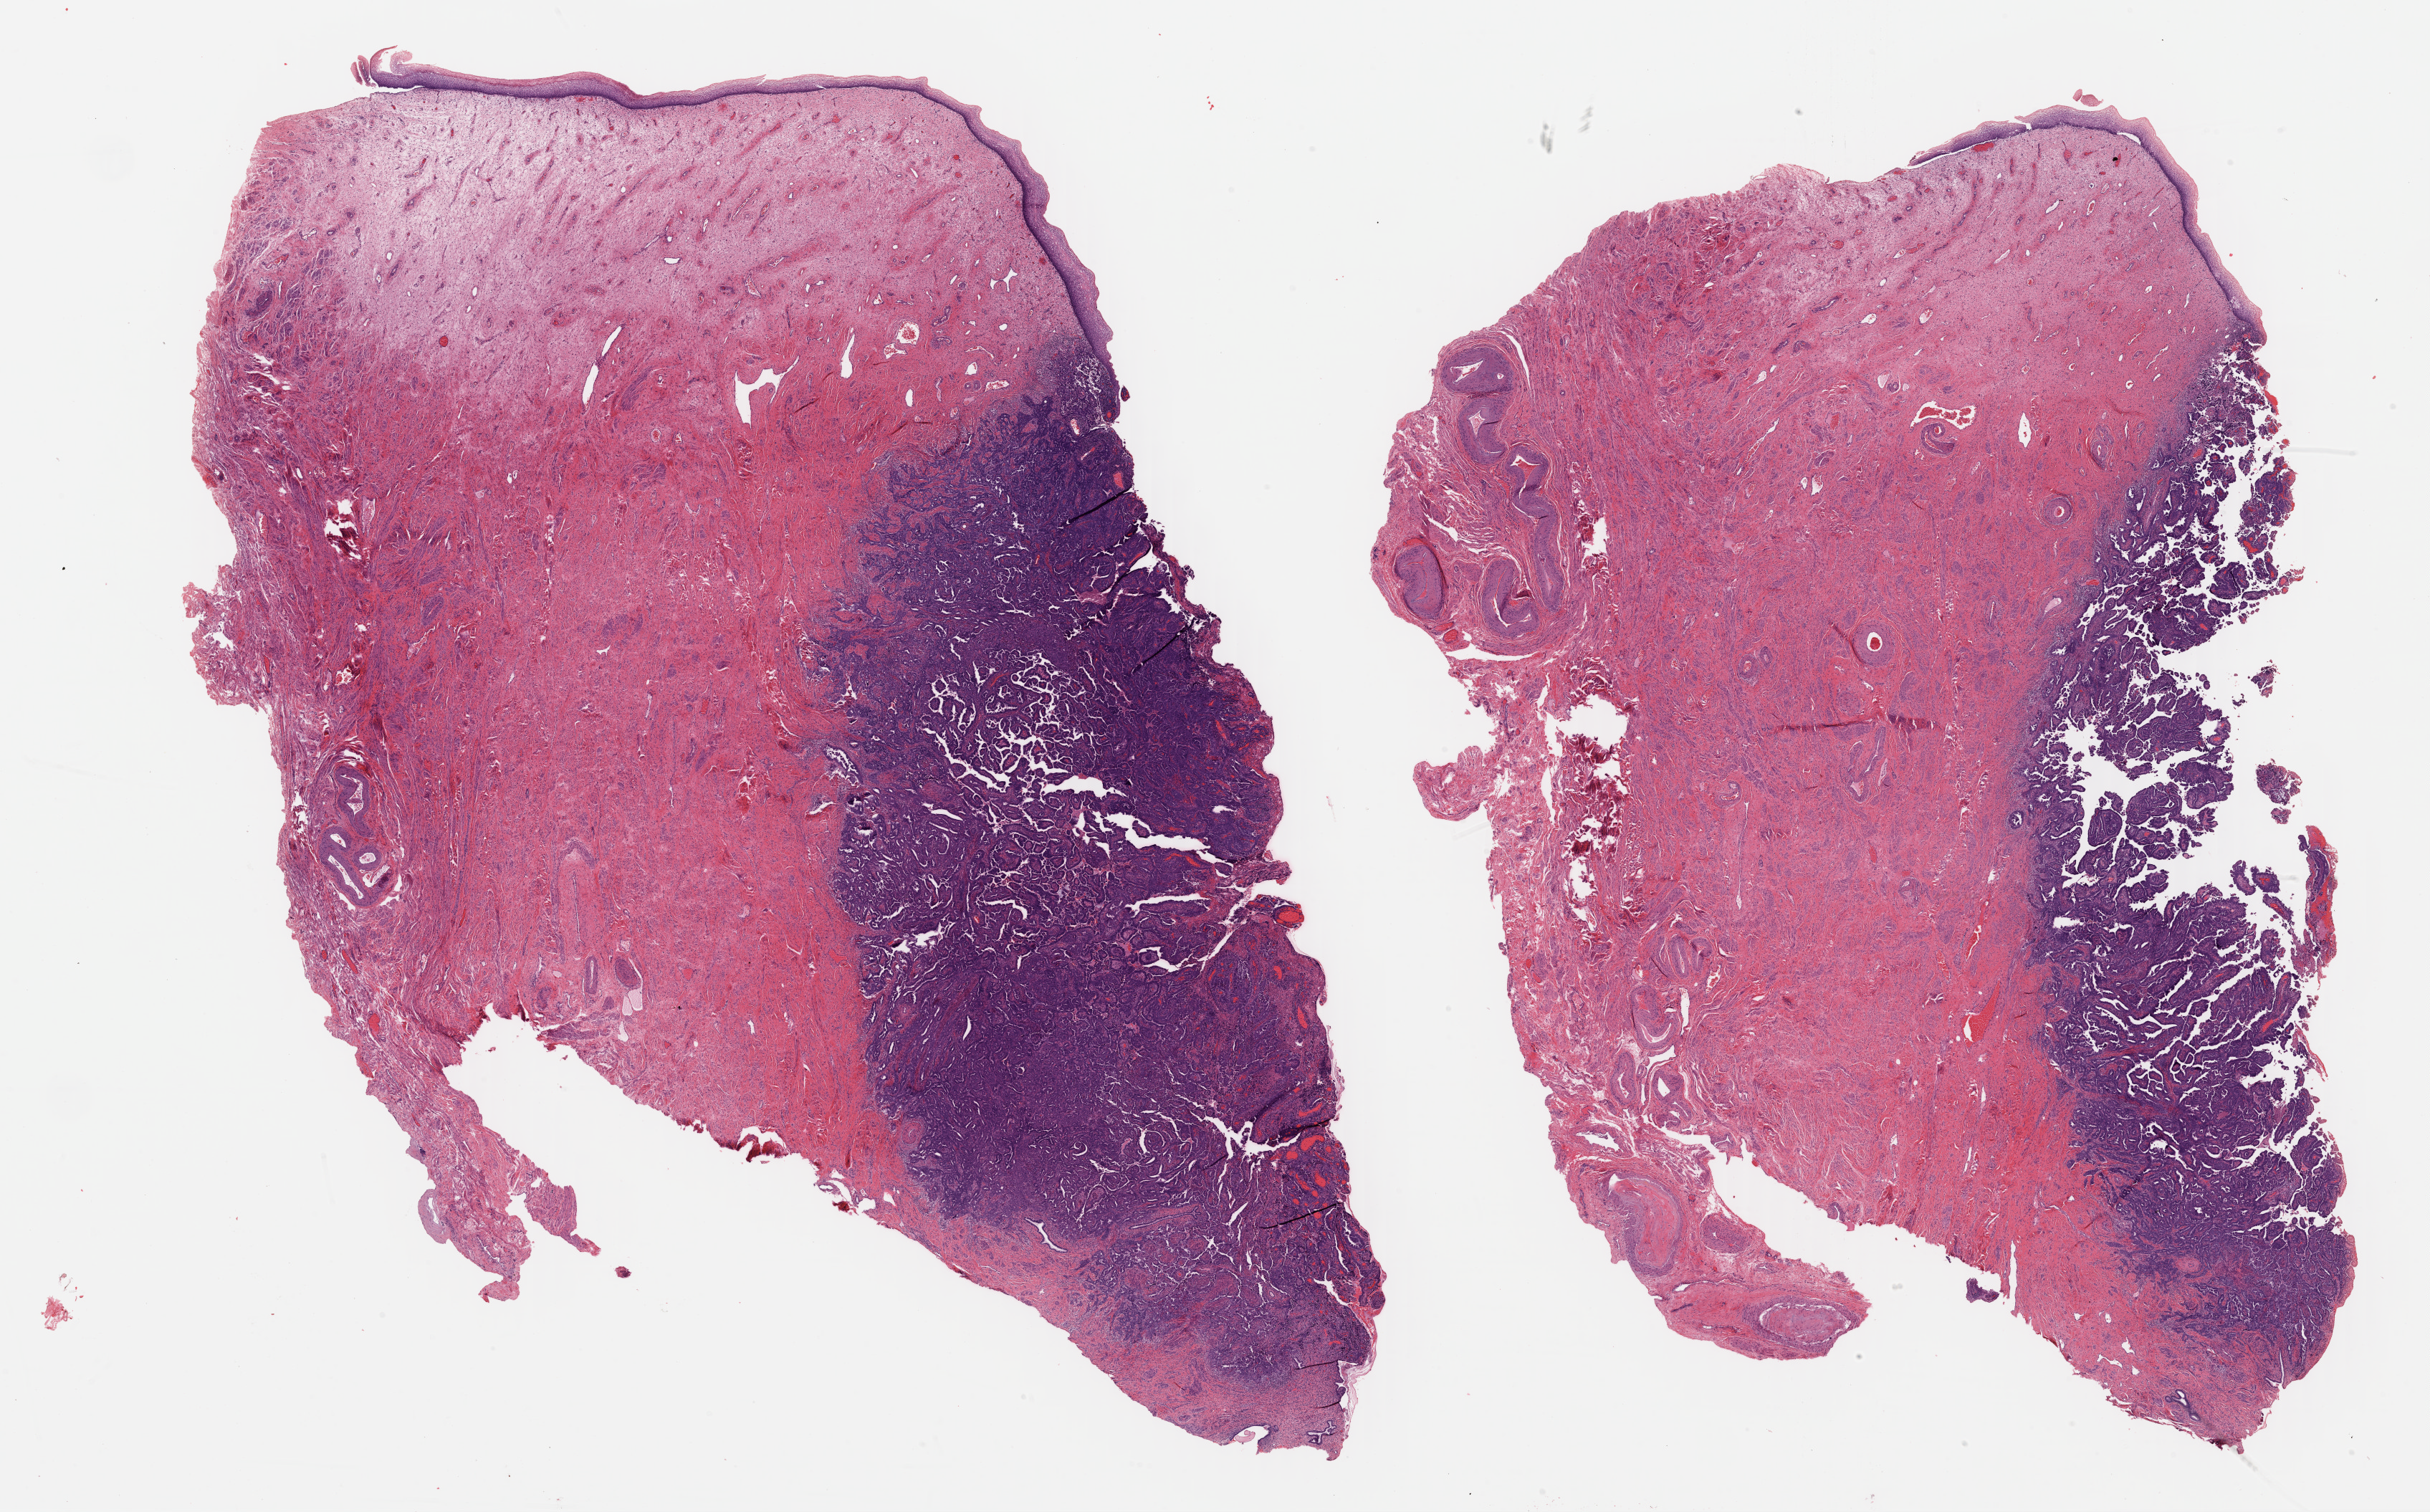
Digitized H&E tissue section (whole slide), whole scanned area (about 26.7 x 16.6 mm, acquisition: 40x scan) shown as a low-resolution overview; formalin-fixed paraffin-embedded (FFPE) diagnostic section; sample: primary tumour, uterus. Female, age 64 years at initial diagnosis.
Diagnosis: Serous cystadenocarcinoma, NOS (endometrium).